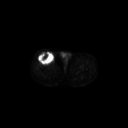
FDG PET of an extremity soft-tissue mass (from a PET/CT study), one axial slice; position 281 of 311 along the scan axis; 3.27 mm slice thickness; 128 × 128 image matrix, field of view 700 × 700 mm. Patient: male, 56 years. From the clinical record (not read from this slice): histological type: pleiomorphic leiomyosarcoma; grade: intermediate; site of the primary tumour: right thigh.
Structures marked on this image (expert contour drawn on MRI and transferred to this co-registered scan by the dataset authors):
- gross tumour volume including surrounding oedema: bounding box [x1, y1, x2, y2] px = [38, 52, 55, 65]
- gross tumour volume (mass): [38, 52, 55, 65]